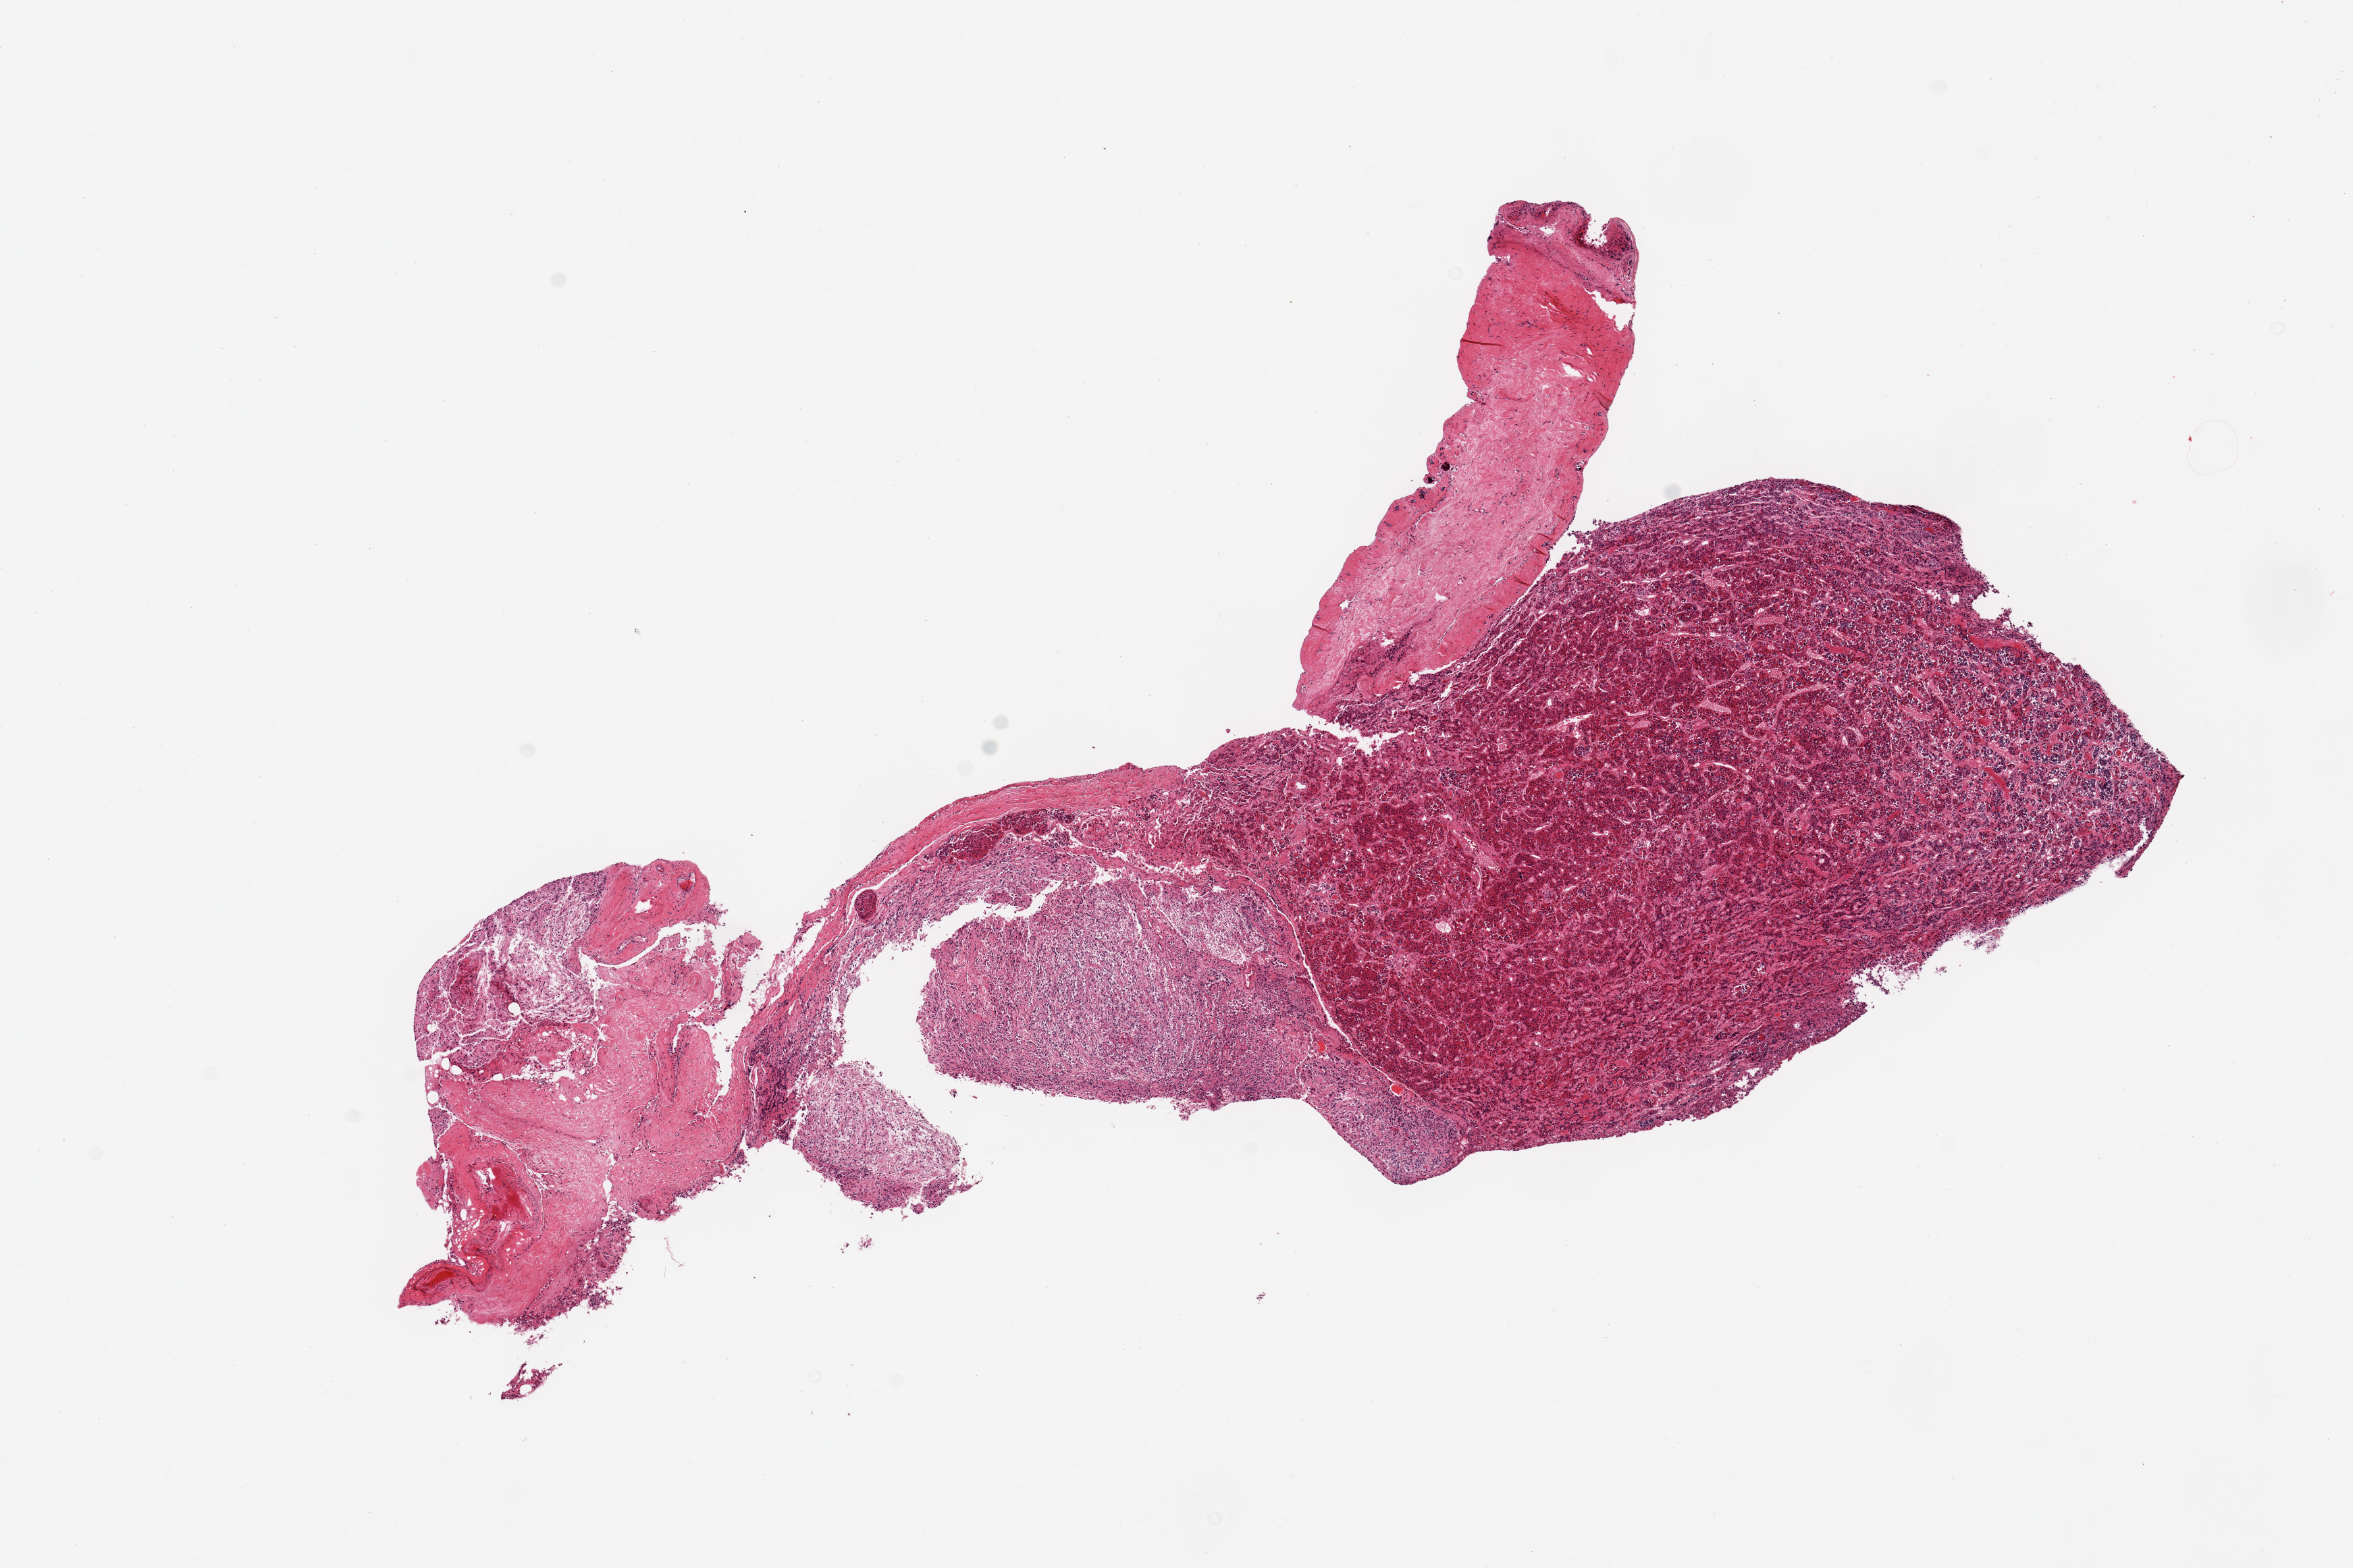
Hematoxylin and eosin (H&E) whole-slide image, whole scanned area (about 13.8 x 9.2 mm, slide scanned at 20x) shown as a low-resolution overview; PAXgene-fixed, paraffin-embedded tissue; target tissue: pituitary; tissue donor sample. Male donor.
Pathologist's review note for this sample: 1 piece, ~20% neurohypophysis; rest is adenohypophysis; adherent dura.